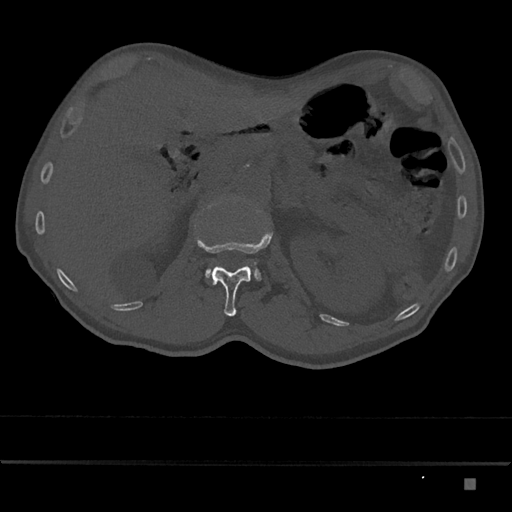
CT including the spine, one axial slice. Position 527 of 797 along the scan axis. 120 kVp. Bone window (W 1800 / L 400 HU). 512 × 512 image matrix. Male patient, age 72 years. Case-level facts recorded for this patient, not image findings: primary cancer: prostate.
Annotated regions visible in this slice (semi-automatically segmented with operator editing):
- L1 vertebra: bounding box <197,203,272,317> (left, top, right, bottom; pixels)
- L2 vertebra: <205,262,261,281>